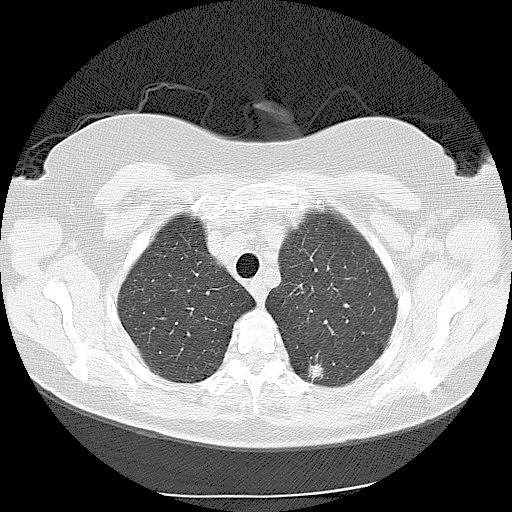
Low-dose screening chest CT, one axial slice; slice 92 of 116 in the series (ordered by position); 120 kVp; lung window (W 1500 / L -600 HU); 512 × 512 image matrix, field of view 360 × 360 mm.
Outlined on this slice (expert manual segmentation):
- lesion 1 (tumor, lower lobe of left lung): box from (x=309, y=364) to (x=324, y=381) px